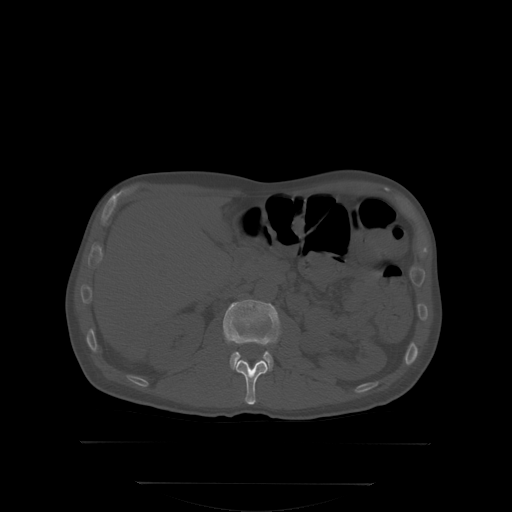
CT including the spine, one axial slice. Position 146 of 350 along the scan axis. Bone window (W 1800 / L 400 HU). 2.5 mm slice thickness. 512 × 512 image matrix, field of view 500 × 500 mm. Patient: male, 58 years. From the clinical record (not read from this slice): primary cancer: prostate; vertebrae with lytic lesions (as recorded): L1.
Annotated regions visible in this slice (semi-automatically segmented with operator editing):
- L1 vertebra: bounding box (x1, y1, x2, y2) in pixels: (235, 359, 268, 405)
- L2 vertebra: (223, 300, 280, 369)